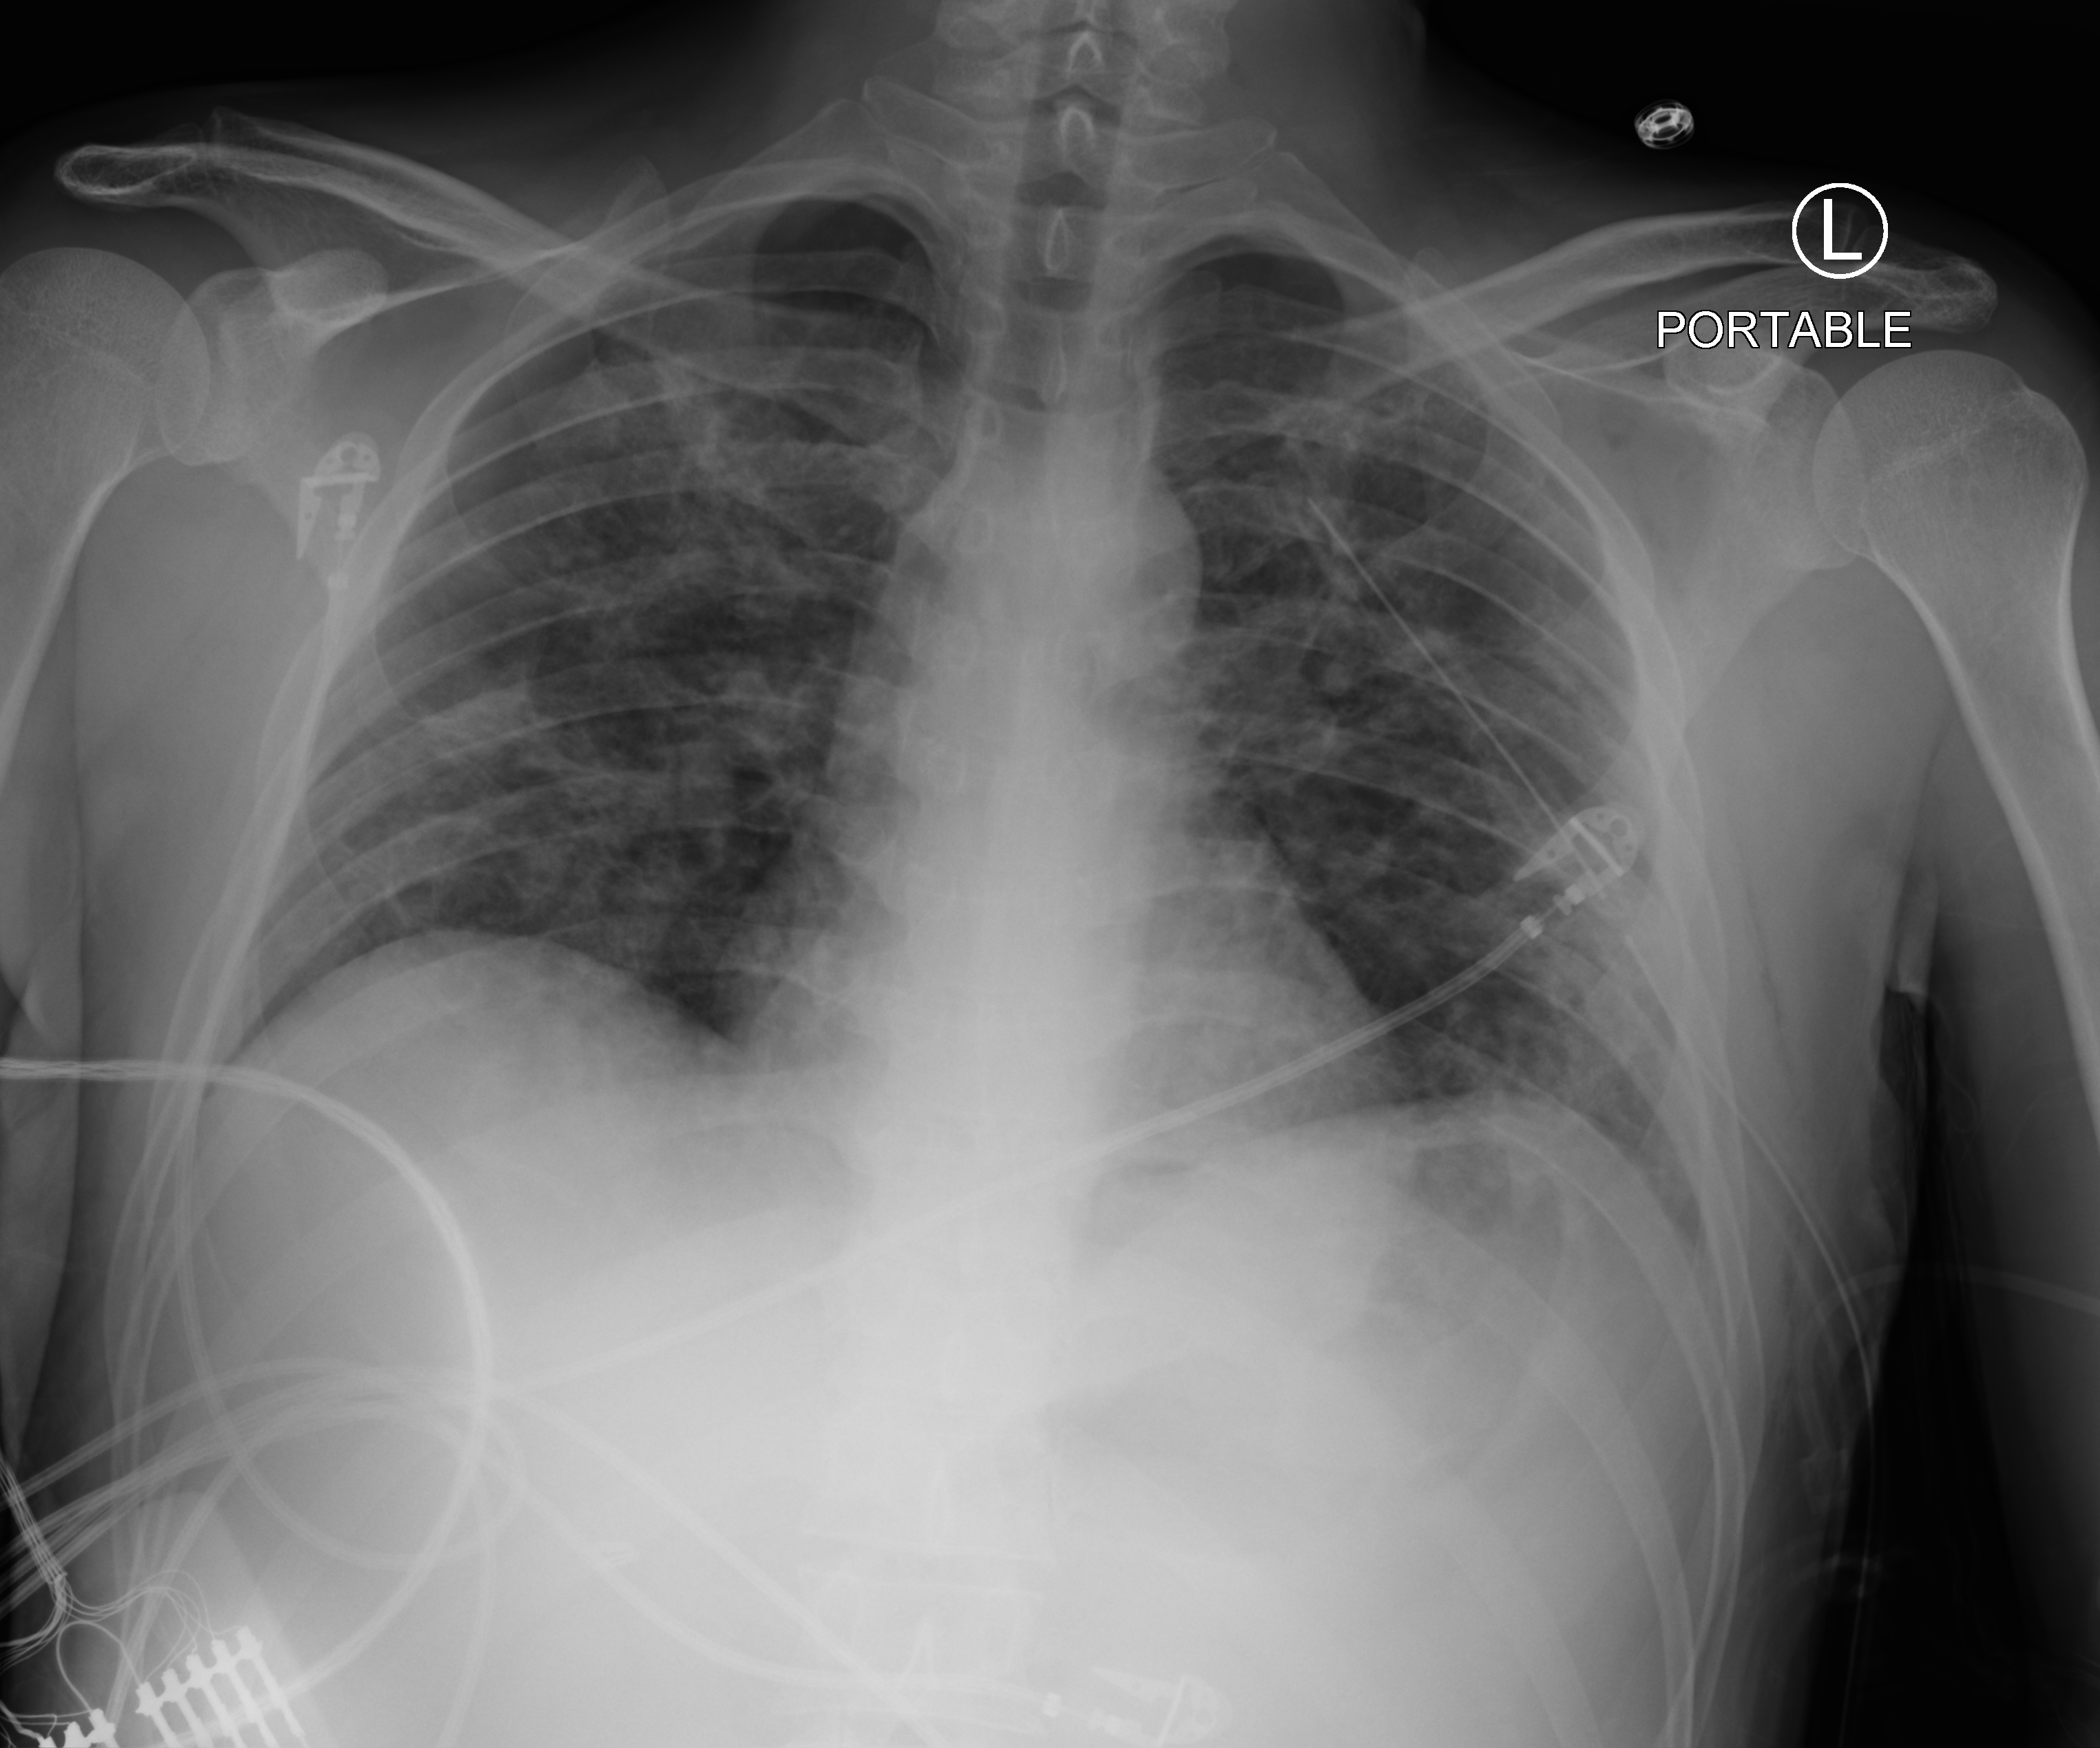
Chest X-ray (portable), anteroposterior (AP) projection. Patient hospitalised with COVID-19; male, aged 18–59 years.
Hospital-stay facts (about this admission, not read from this image; timing relative to this image not recorded):
- admitted to intensive care during this hospital stay: yes